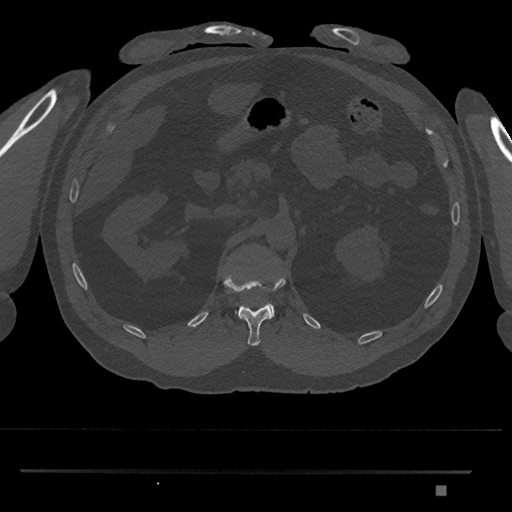
CT including the spine, one axial slice; position 866 of 1134 along the scan axis; reconstruction kernel Br40s/3; bone window (W 1800 / L 400 HU); 512 × 512 image matrix, field of view 429 × 429 mm. Male patient, age 65 years. From the clinical record (not read from this slice): primary cancer: prostate.
Outlined on this slice (semi-automatic segmentation, software-assisted and operator-edited):
- L1 vertebra: bounding box <235,304,275,318> (left, top, right, bottom; pixels)
- T12 vertebra: <223,272,286,346>